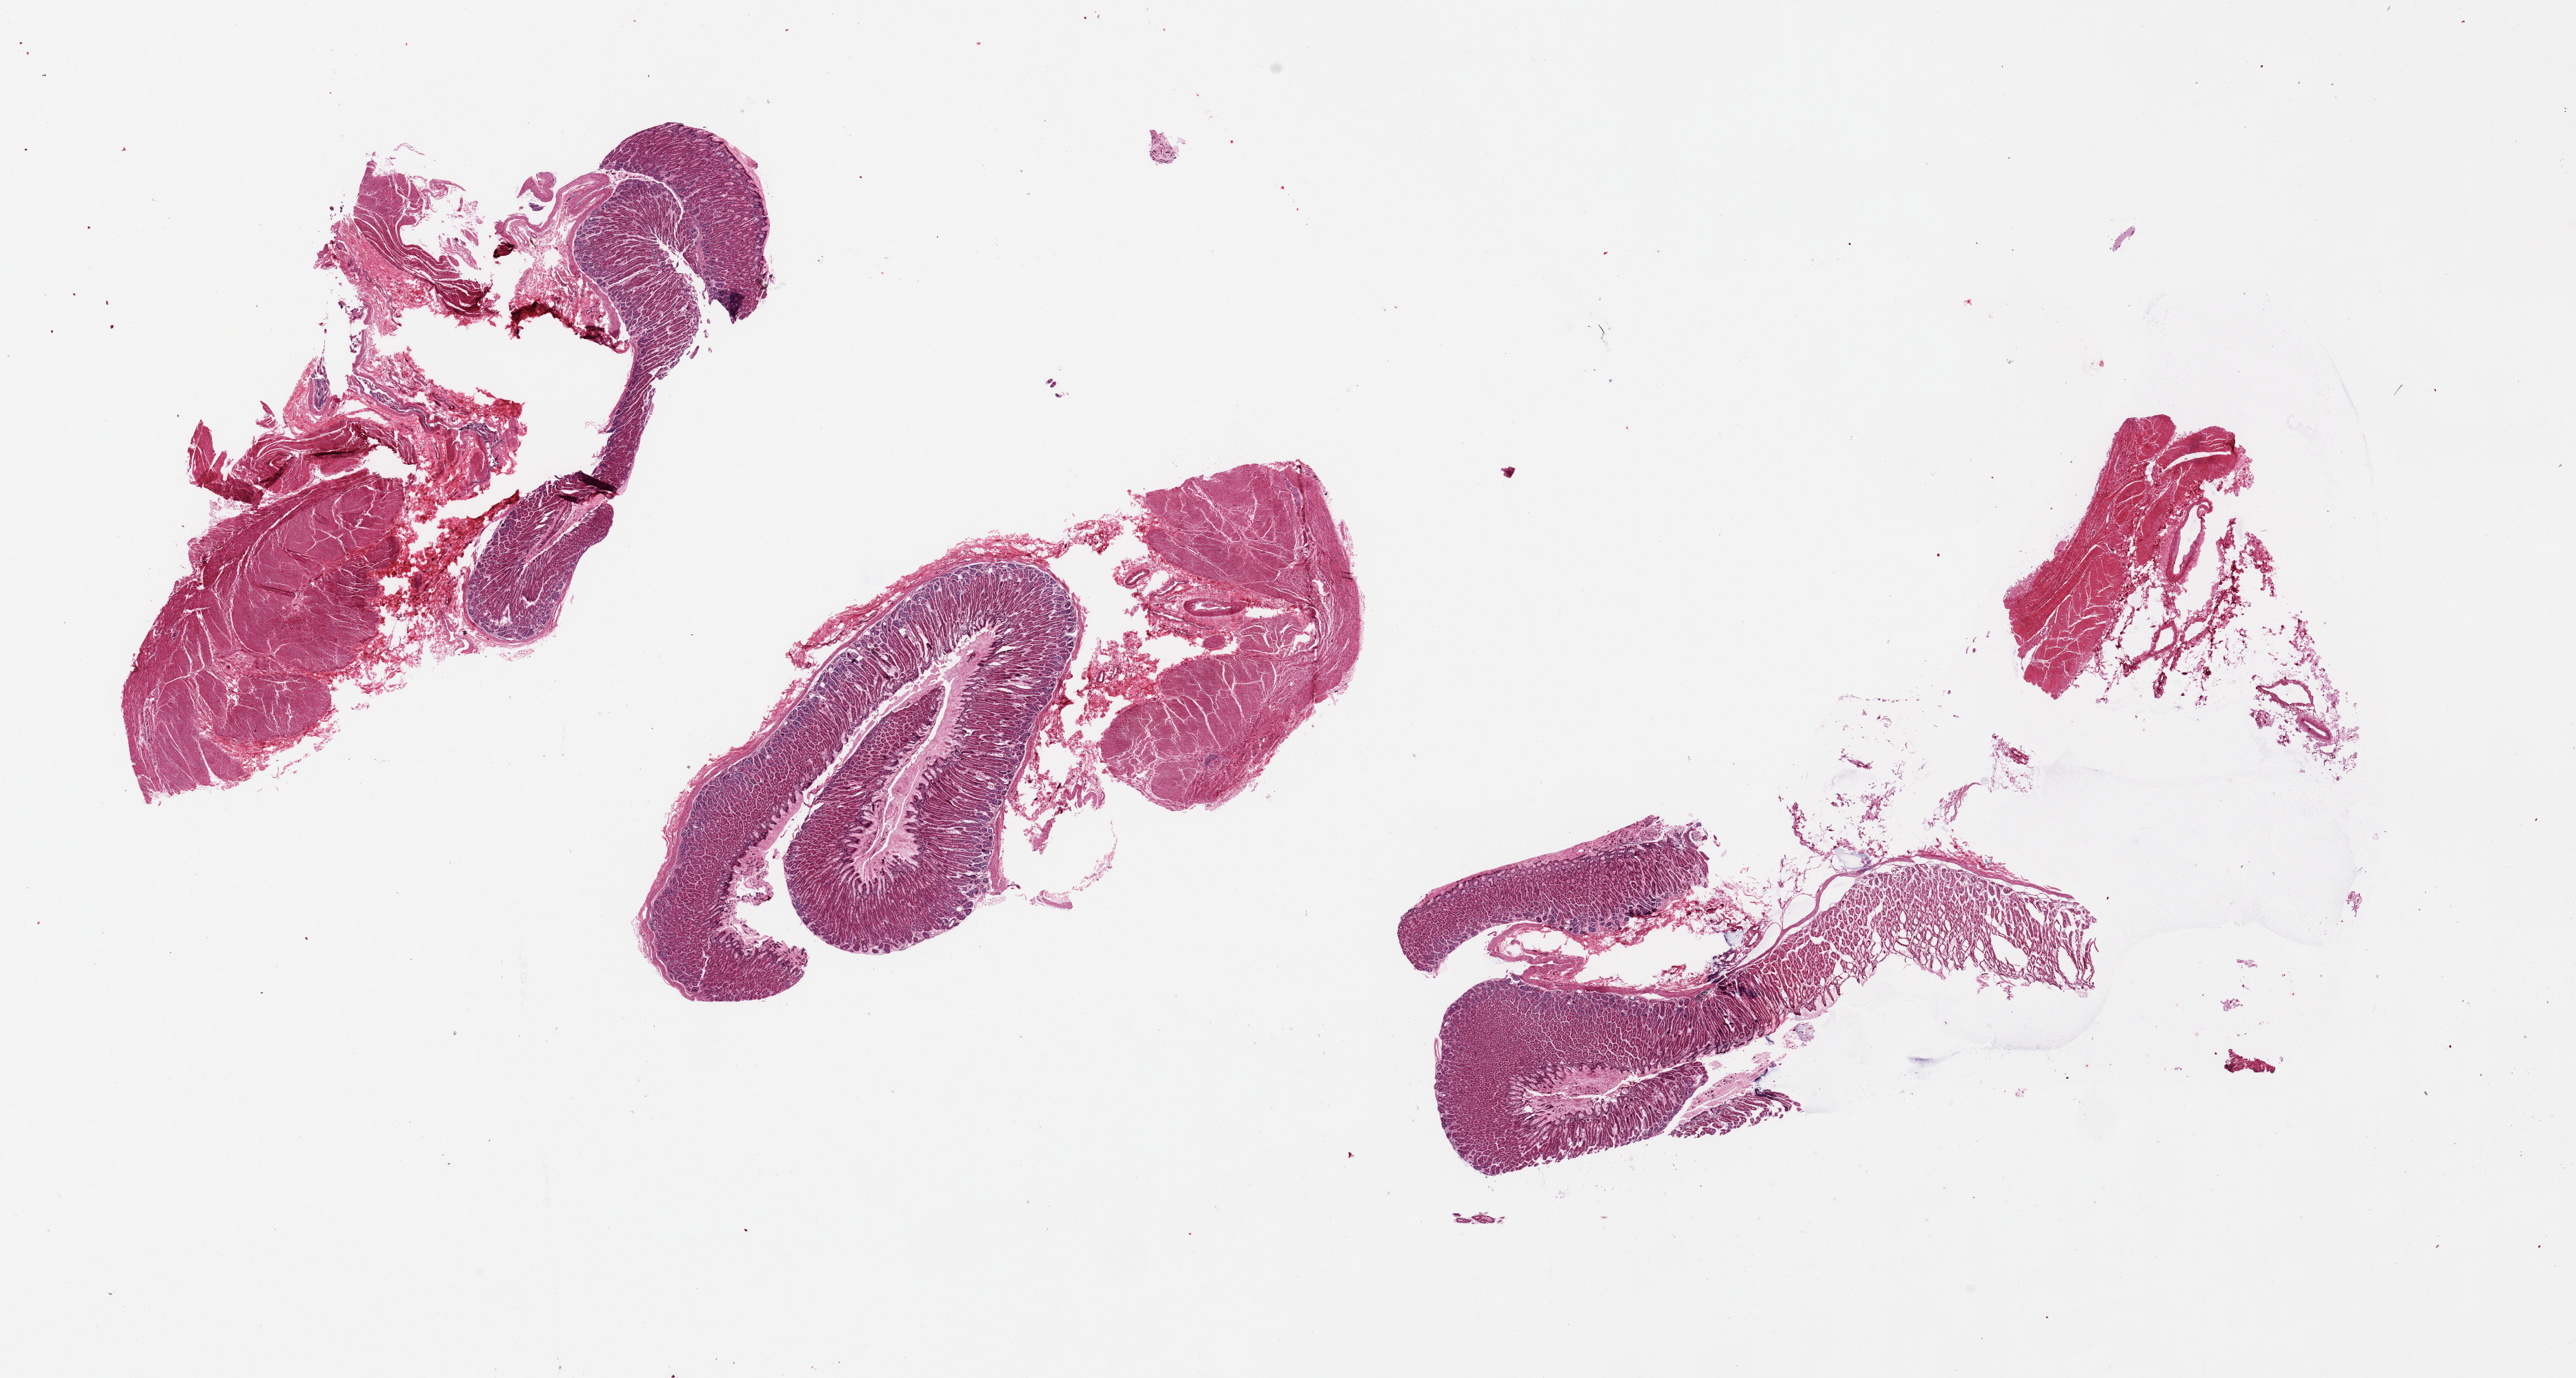
Digitized haematoxylin and eosin-stained section, low-resolution overview of the scanned area, about 29.5 x 15.8 mm; PAXgene-fixed, paraffin-embedded tissue; sampled site (target tissue): stomach; donor tissue sample. Male donor.
* pathologist's review note for this sample: Some areas approach 0???remarkably well-preserved. Approximately 50% of specimen is ???pure??? mucosa